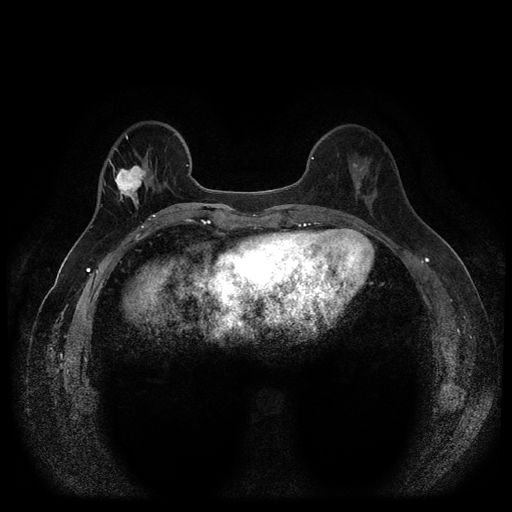
Breast MRI (dynamic contrast-enhanced, multi-phase), one axial slice; slice 33 of 116 in the series (ordered by position); dynamic contrast-enhanced series, time point 2 of 5 at this slice position (early post-contrast); 1.5 T; TE 2.6 ms, TR 5.4 ms; 2 mm slice thickness; 512 × 512 image matrix. Patient: female, 56 years.
Structures marked on this image (semi-automatic segmentation, software-assisted and operator-edited):
- breast lesion (labelled 'tumour' in the annotation; benign lesions carry a separate 'benign' label): bounding box [x1, y1, x2, y2] px = [108, 157, 151, 211]